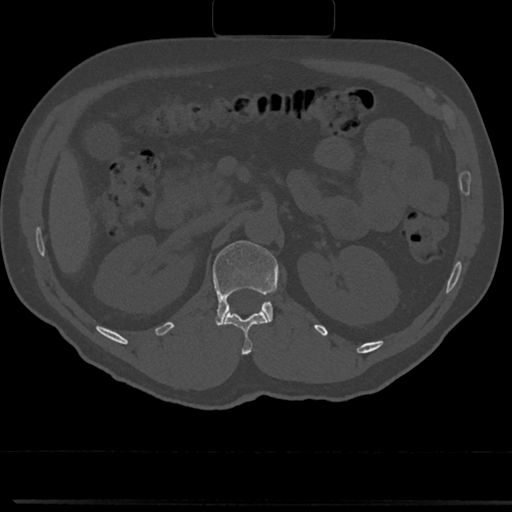
CT including the spine, one axial slice. Slice 106 of 817 in the series (ordered by position). Reconstruction kernel Br40s/3. Bone window (W 1800 / L 400 HU). 512 × 512 image matrix. Male patient, age 61 years. Case-level facts recorded for this patient, not image findings: primary cancer: prostate.
Outlined on this slice (semi-automatic segmentation, software-assisted and operator-edited):
- L1 vertebra: bounding box <192,240,278,326> (left, top, right, bottom; pixels)
- T12 vertebra: <224,311,268,353>